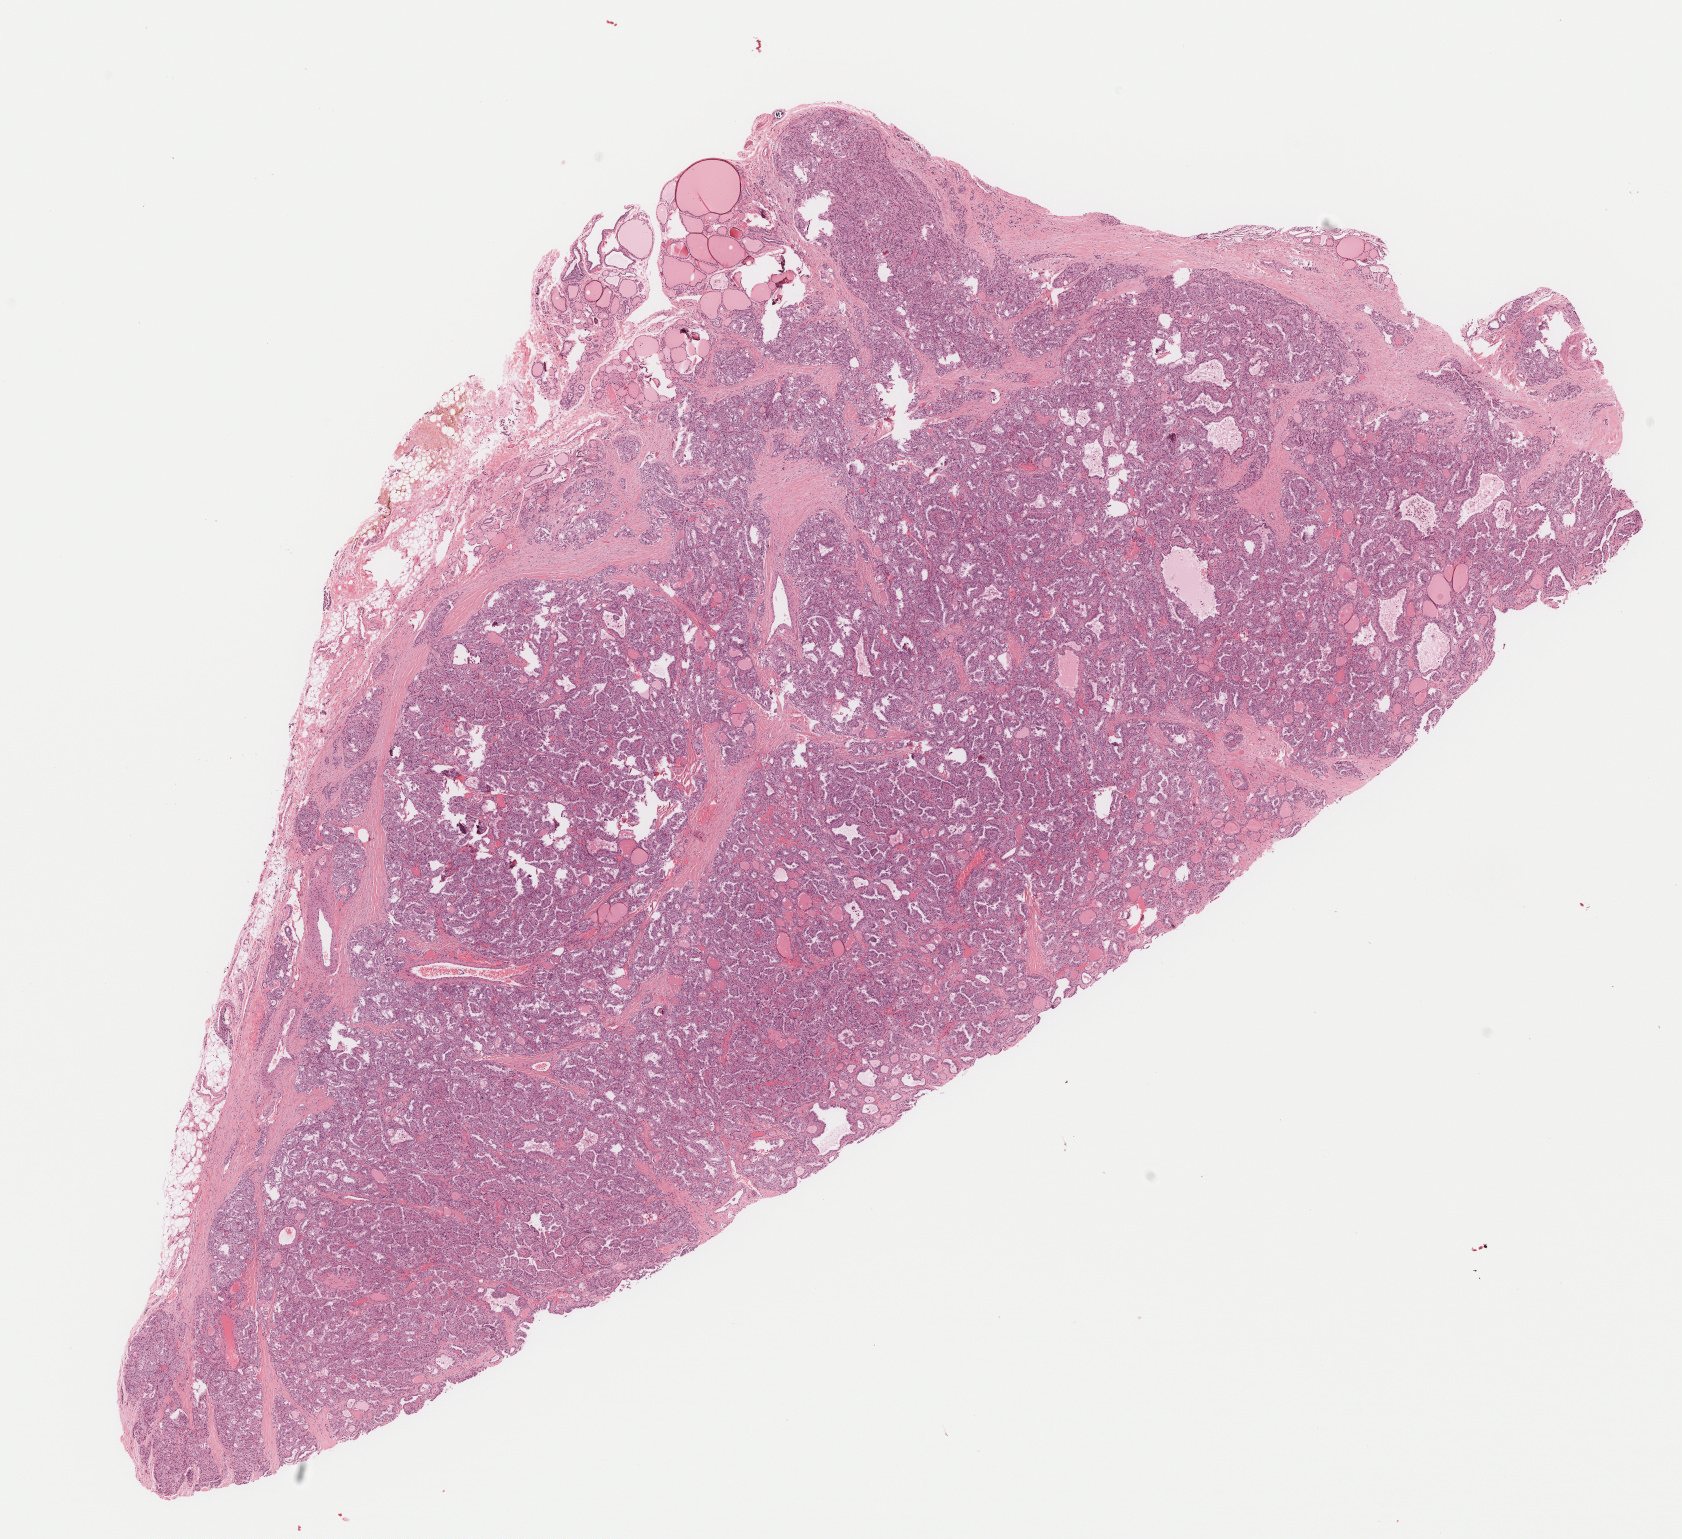
H&E whole-slide image, low-resolution overview of the scanned area, about 13.5 x 12.4 mm (from a 40x scan). Formalin-fixed paraffin-embedded (FFPE) diagnostic section. Primary tumour sample from the thyroid. Patient: male, age at initial diagnosis 46 years.
Lymph nodes positive (case pathology): 8 of 9 examined. AJCC pathologic stage: IVA (7th edition). Pathologic diagnosis: Papillary adenocarcinoma, NOS (thyroid gland). Laterality: right.